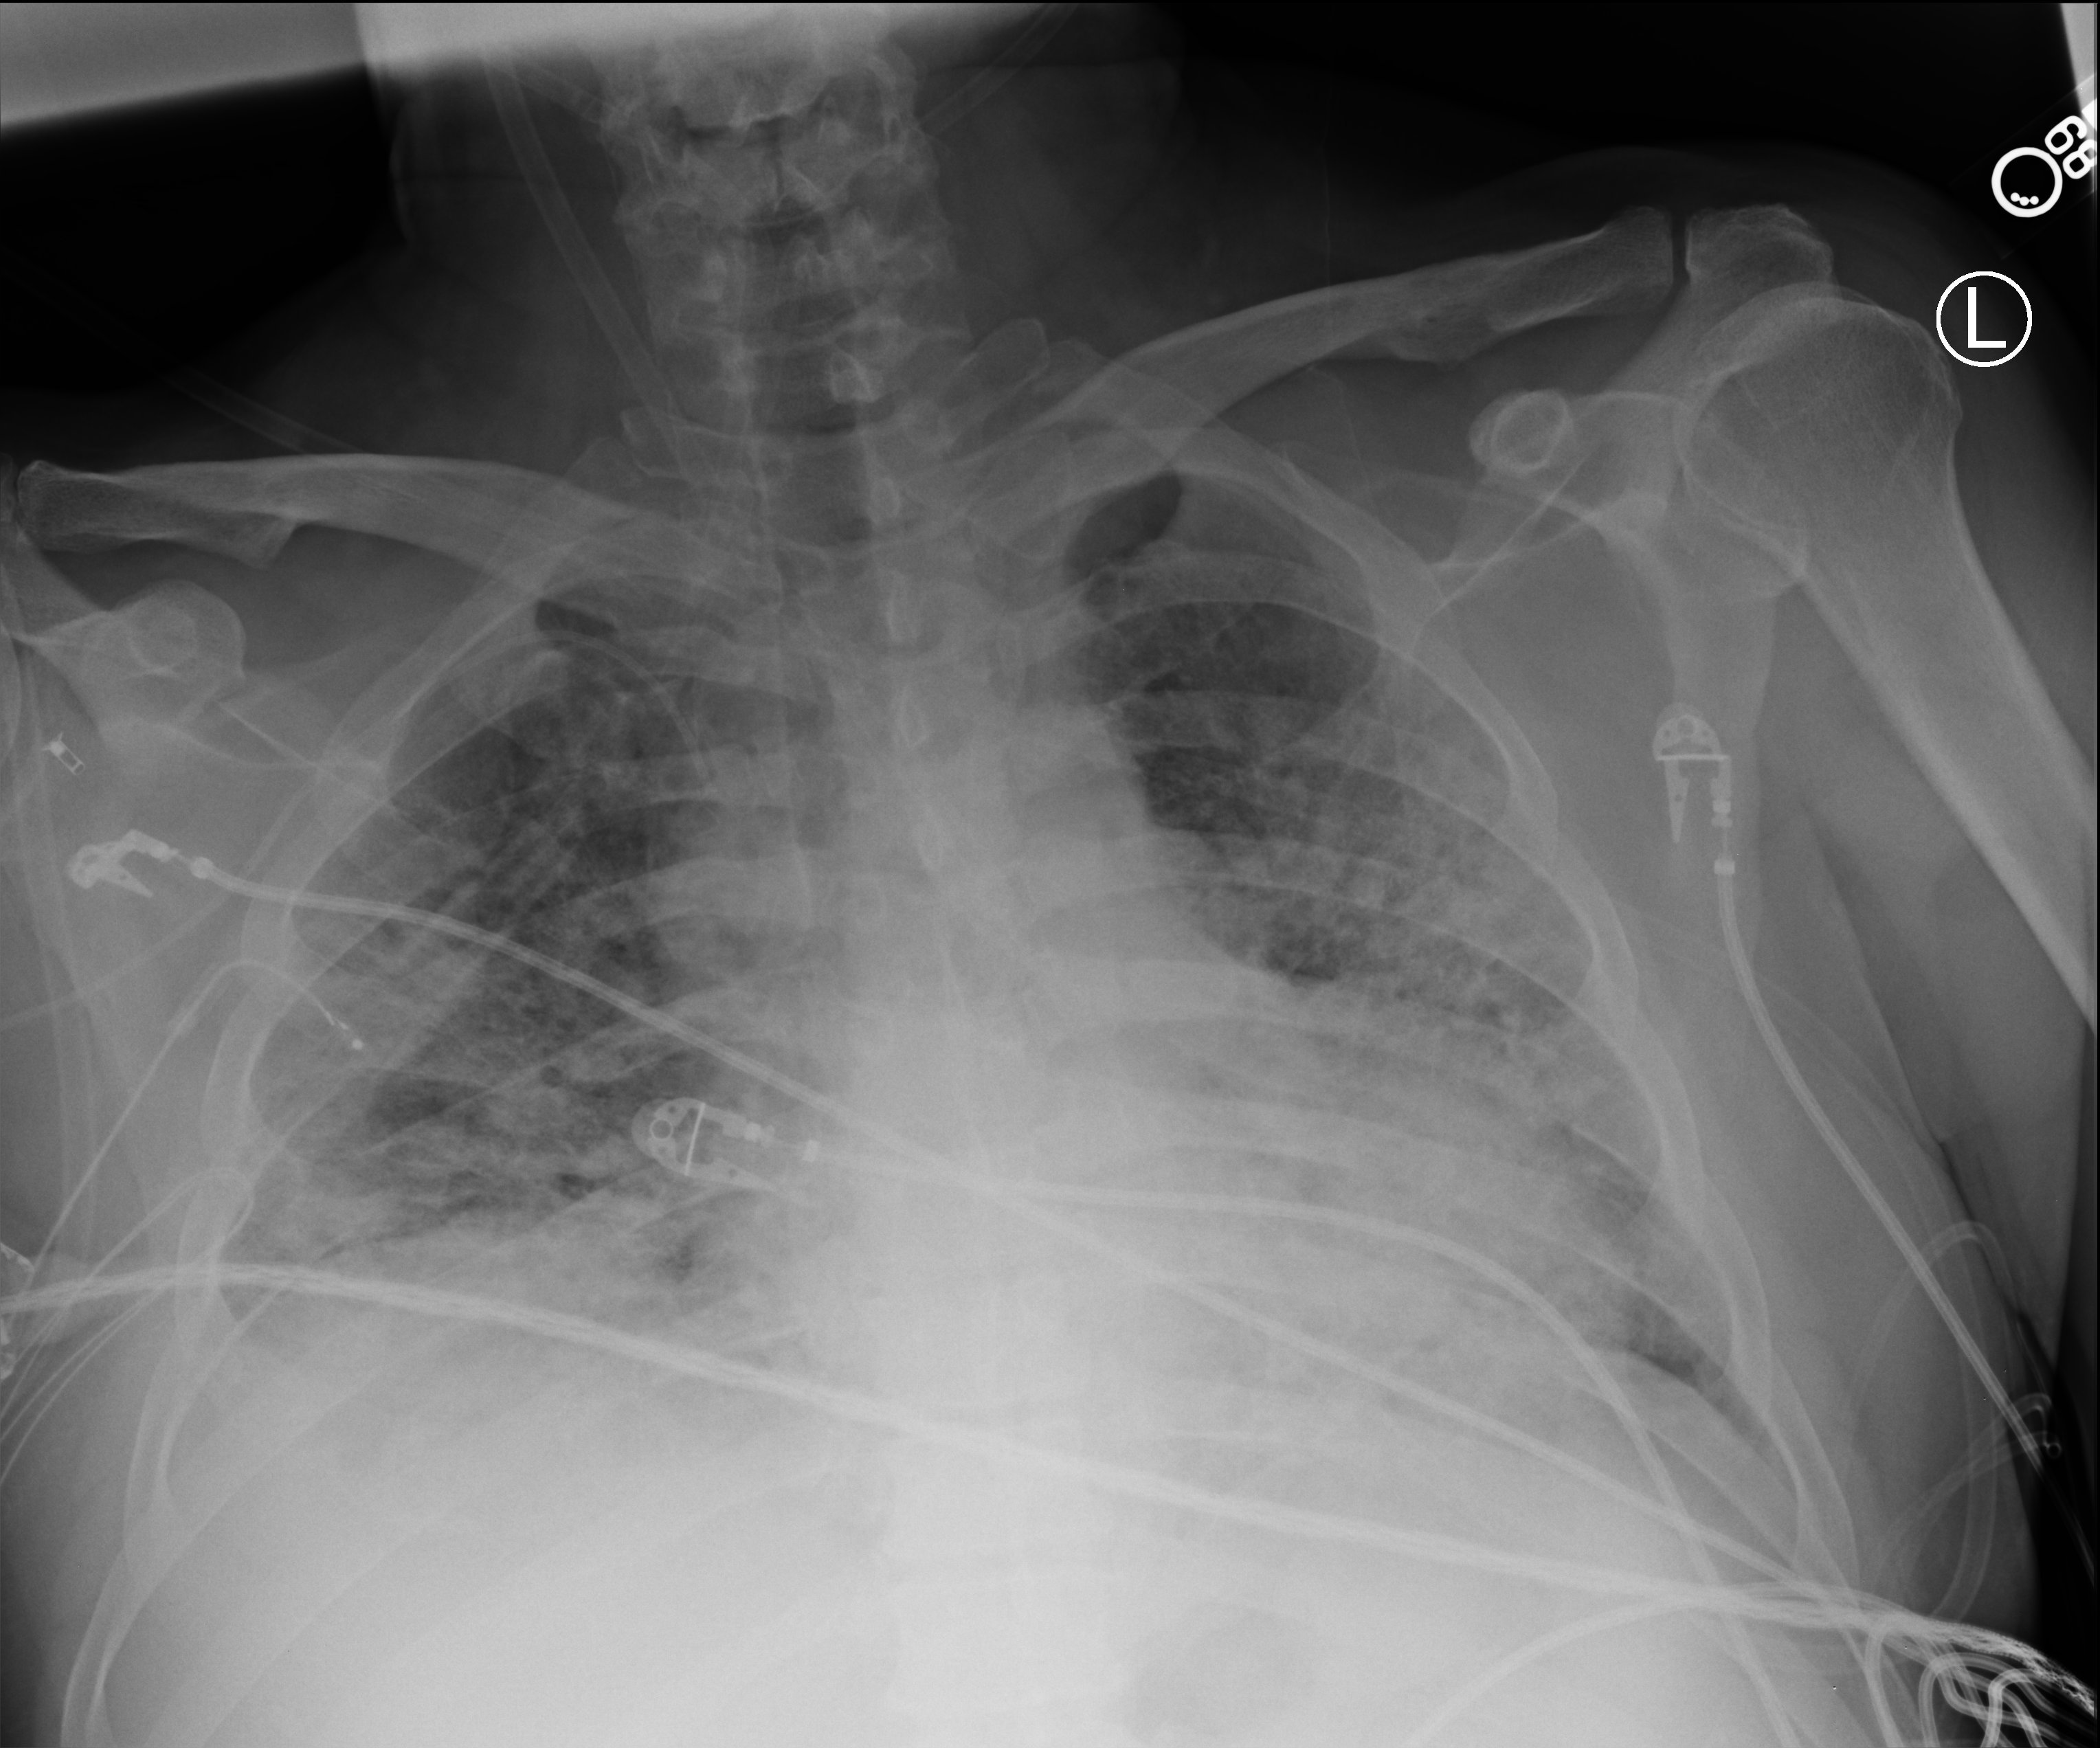
Bedside chest radiograph (computed radiography); anteroposterior (AP) projection. Patient hospitalised with COVID-19; male, aged 18–59 years.
Admission-level facts for this patient (not findings on this image; timing relative to this image not recorded):
- hypertension (admission record): no
- diabetes (admission record): no
- length of hospital stay: 52 days